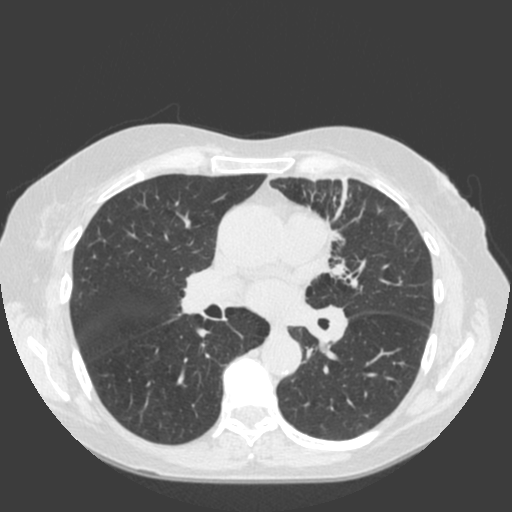
Low-dose screening chest CT, one axial slice. Slice 105 of 184 in the series (ordered by position). Lung window (W 1500 / L -600 HU). 2 mm slice thickness. 512 × 512 image matrix.
Outlined on this slice (expert manual segmentation):
- lesion 1 (tumor, hilum of left lung): bounding box [x1, y1, x2, y2] px = [330, 231, 361, 289]